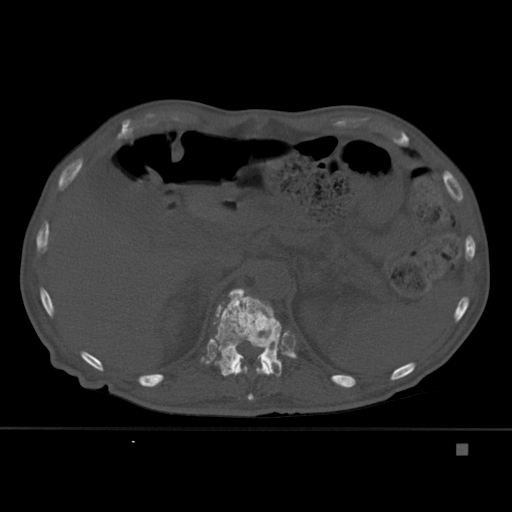
CT including the spine, one axial slice. Slice 205 of 451 in the series (ordered by position). Bone window (W 1800 / L 400 HU). 1.5 mm slice thickness. 512 × 512 image matrix, field of view 378 × 378 mm. Male patient, age 75 years. Case-level facts recorded for this patient, not image findings: primary cancer: prostate.
Outlined on this slice (semi-automatic segmentation, software-assisted and operator-edited):
- T11 vertebra: bounding box <232,357,272,400> (left, top, right, bottom; pixels)
- T12 vertebra: <211,288,282,377>